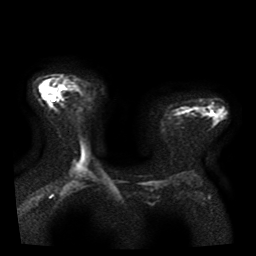
Breast MRI, one axial slice; slice 27 of 41 in the series (ordered by position); diffusion-weighted series; image 2 of 4 stored at this slice position (different b-values; order by instance number); 1.5 T; 5 mm slice thickness; 256 × 256 image matrix. Female patient.
Outlined on this slice (outlined manually by an expert reader):
- tumour on diffusion-weighted imaging: bounding box <57,92,60,96> (left, top, right, bottom; pixels)